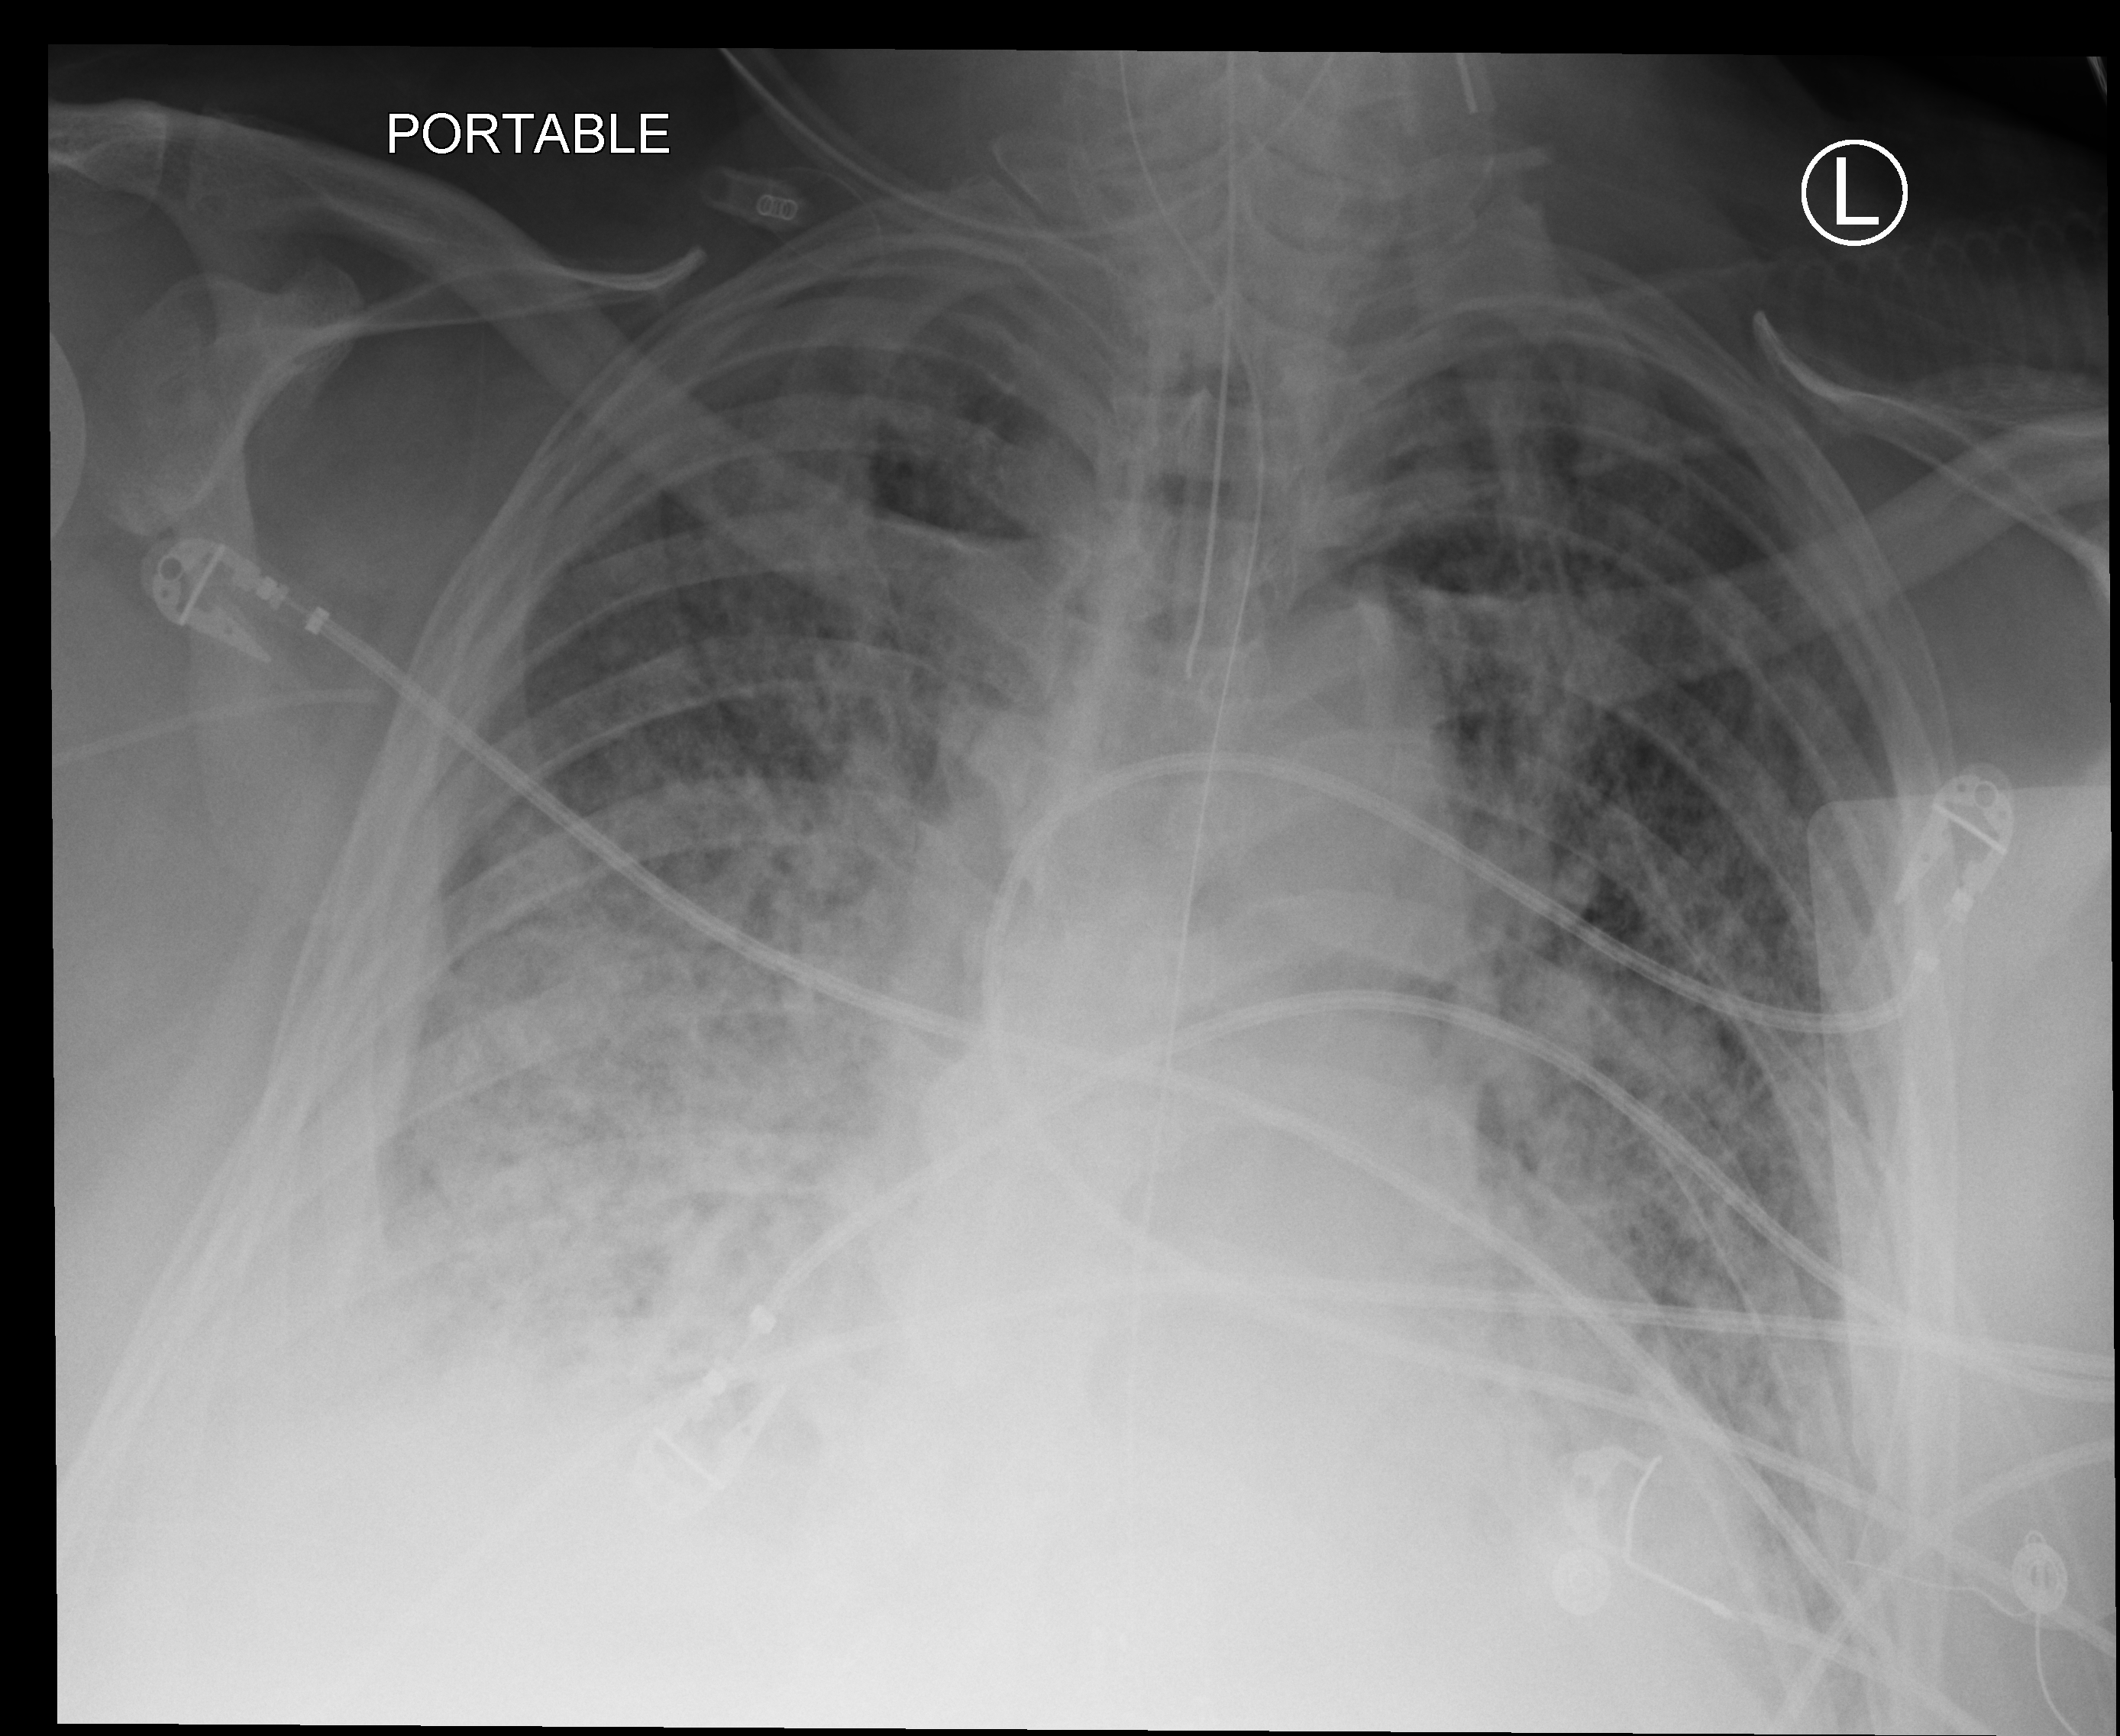
Portable chest radiograph, anteroposterior (AP) projection. Patient hospitalised with COVID-19; male, aged 60–74 years.
Admission-level facts for this patient (not findings on this image; timing relative to this image not recorded): admitted to intensive care during this hospital stay: yes; length of hospital stay: 40 days.